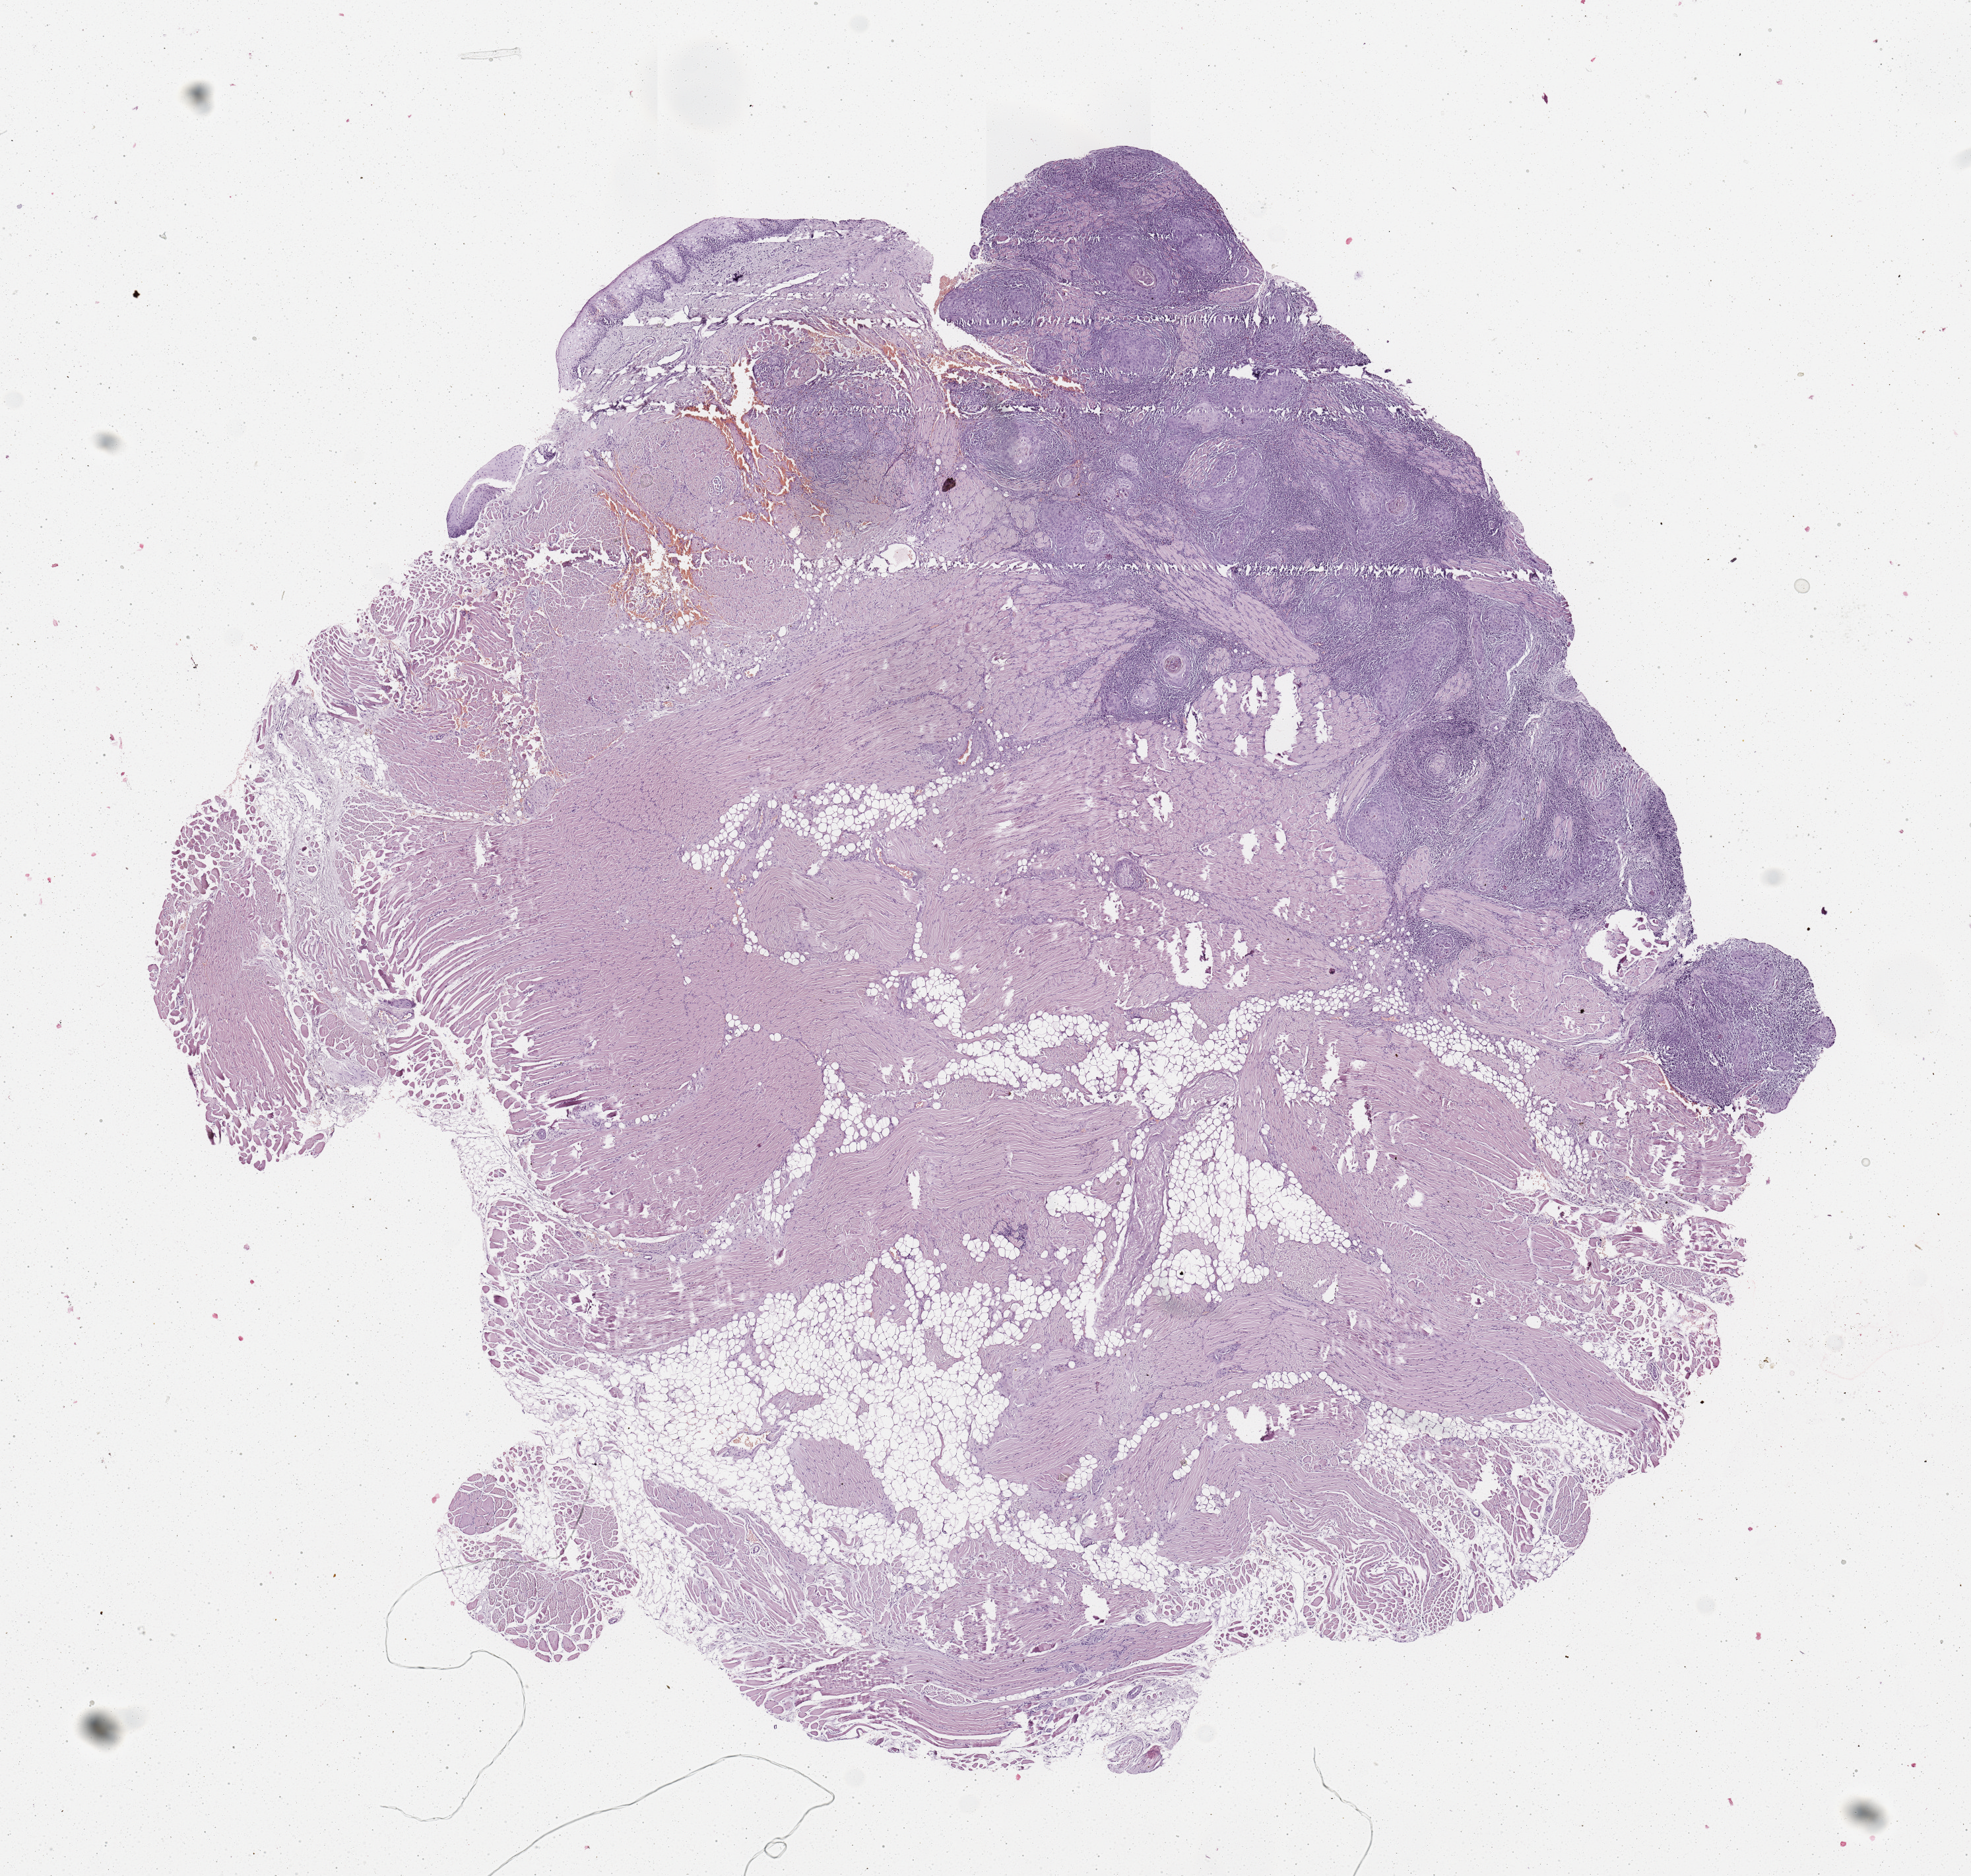
Digitized Hematoxylin and eosin (H&E) stained tissue section (whole slide) — a low-resolution overview of the entire scanned area, about 11.8 x 11.2 mm (acquisition: 20x scan). Head and neck, tissue type not recorded. Patient: male, age 61 years.
- patient diagnosis: Squamous cell carcinoma, NOS (tongue, NOS)